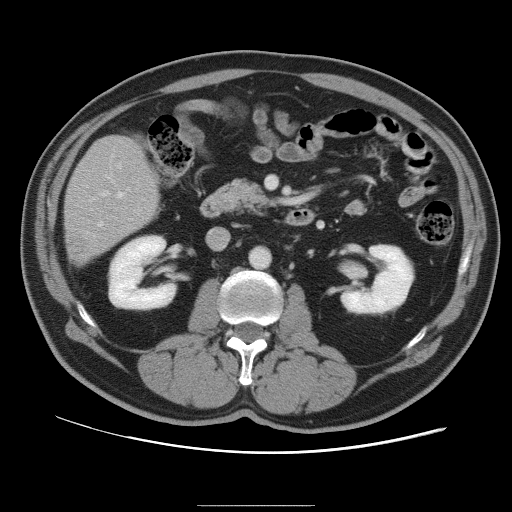
Contrast-enhanced abdominal CT, one axial slice; slice 37 of 105 in the series (ordered by position); intravenous contrast given; soft-tissue window (W 400 / L 40 HU); 5 mm slice thickness; 512 × 512 image matrix, field of view 399 × 399 mm. Male patient, age 64 years. From the clinical record (not read from this slice): diagnosis: colorectal cancer liver metastases, imaged before liver resection; multiple liver metastases: yes; largest metastasis: 3 cm; chemotherapy before resection: yes.
Structures marked on this image (manually delineated by an expert):
- hepatic veins: bounding box (x1, y1, x2, y2) in pixels: (99, 192, 123, 226)
- liver: (65, 137, 160, 263)
- planned liver remnant (the part of the liver to remain after resection): (66, 137, 159, 240)
- portal vein (with intrahepatic branches): (101, 164, 121, 196)
- liver metastasis: (70, 238, 86, 258)